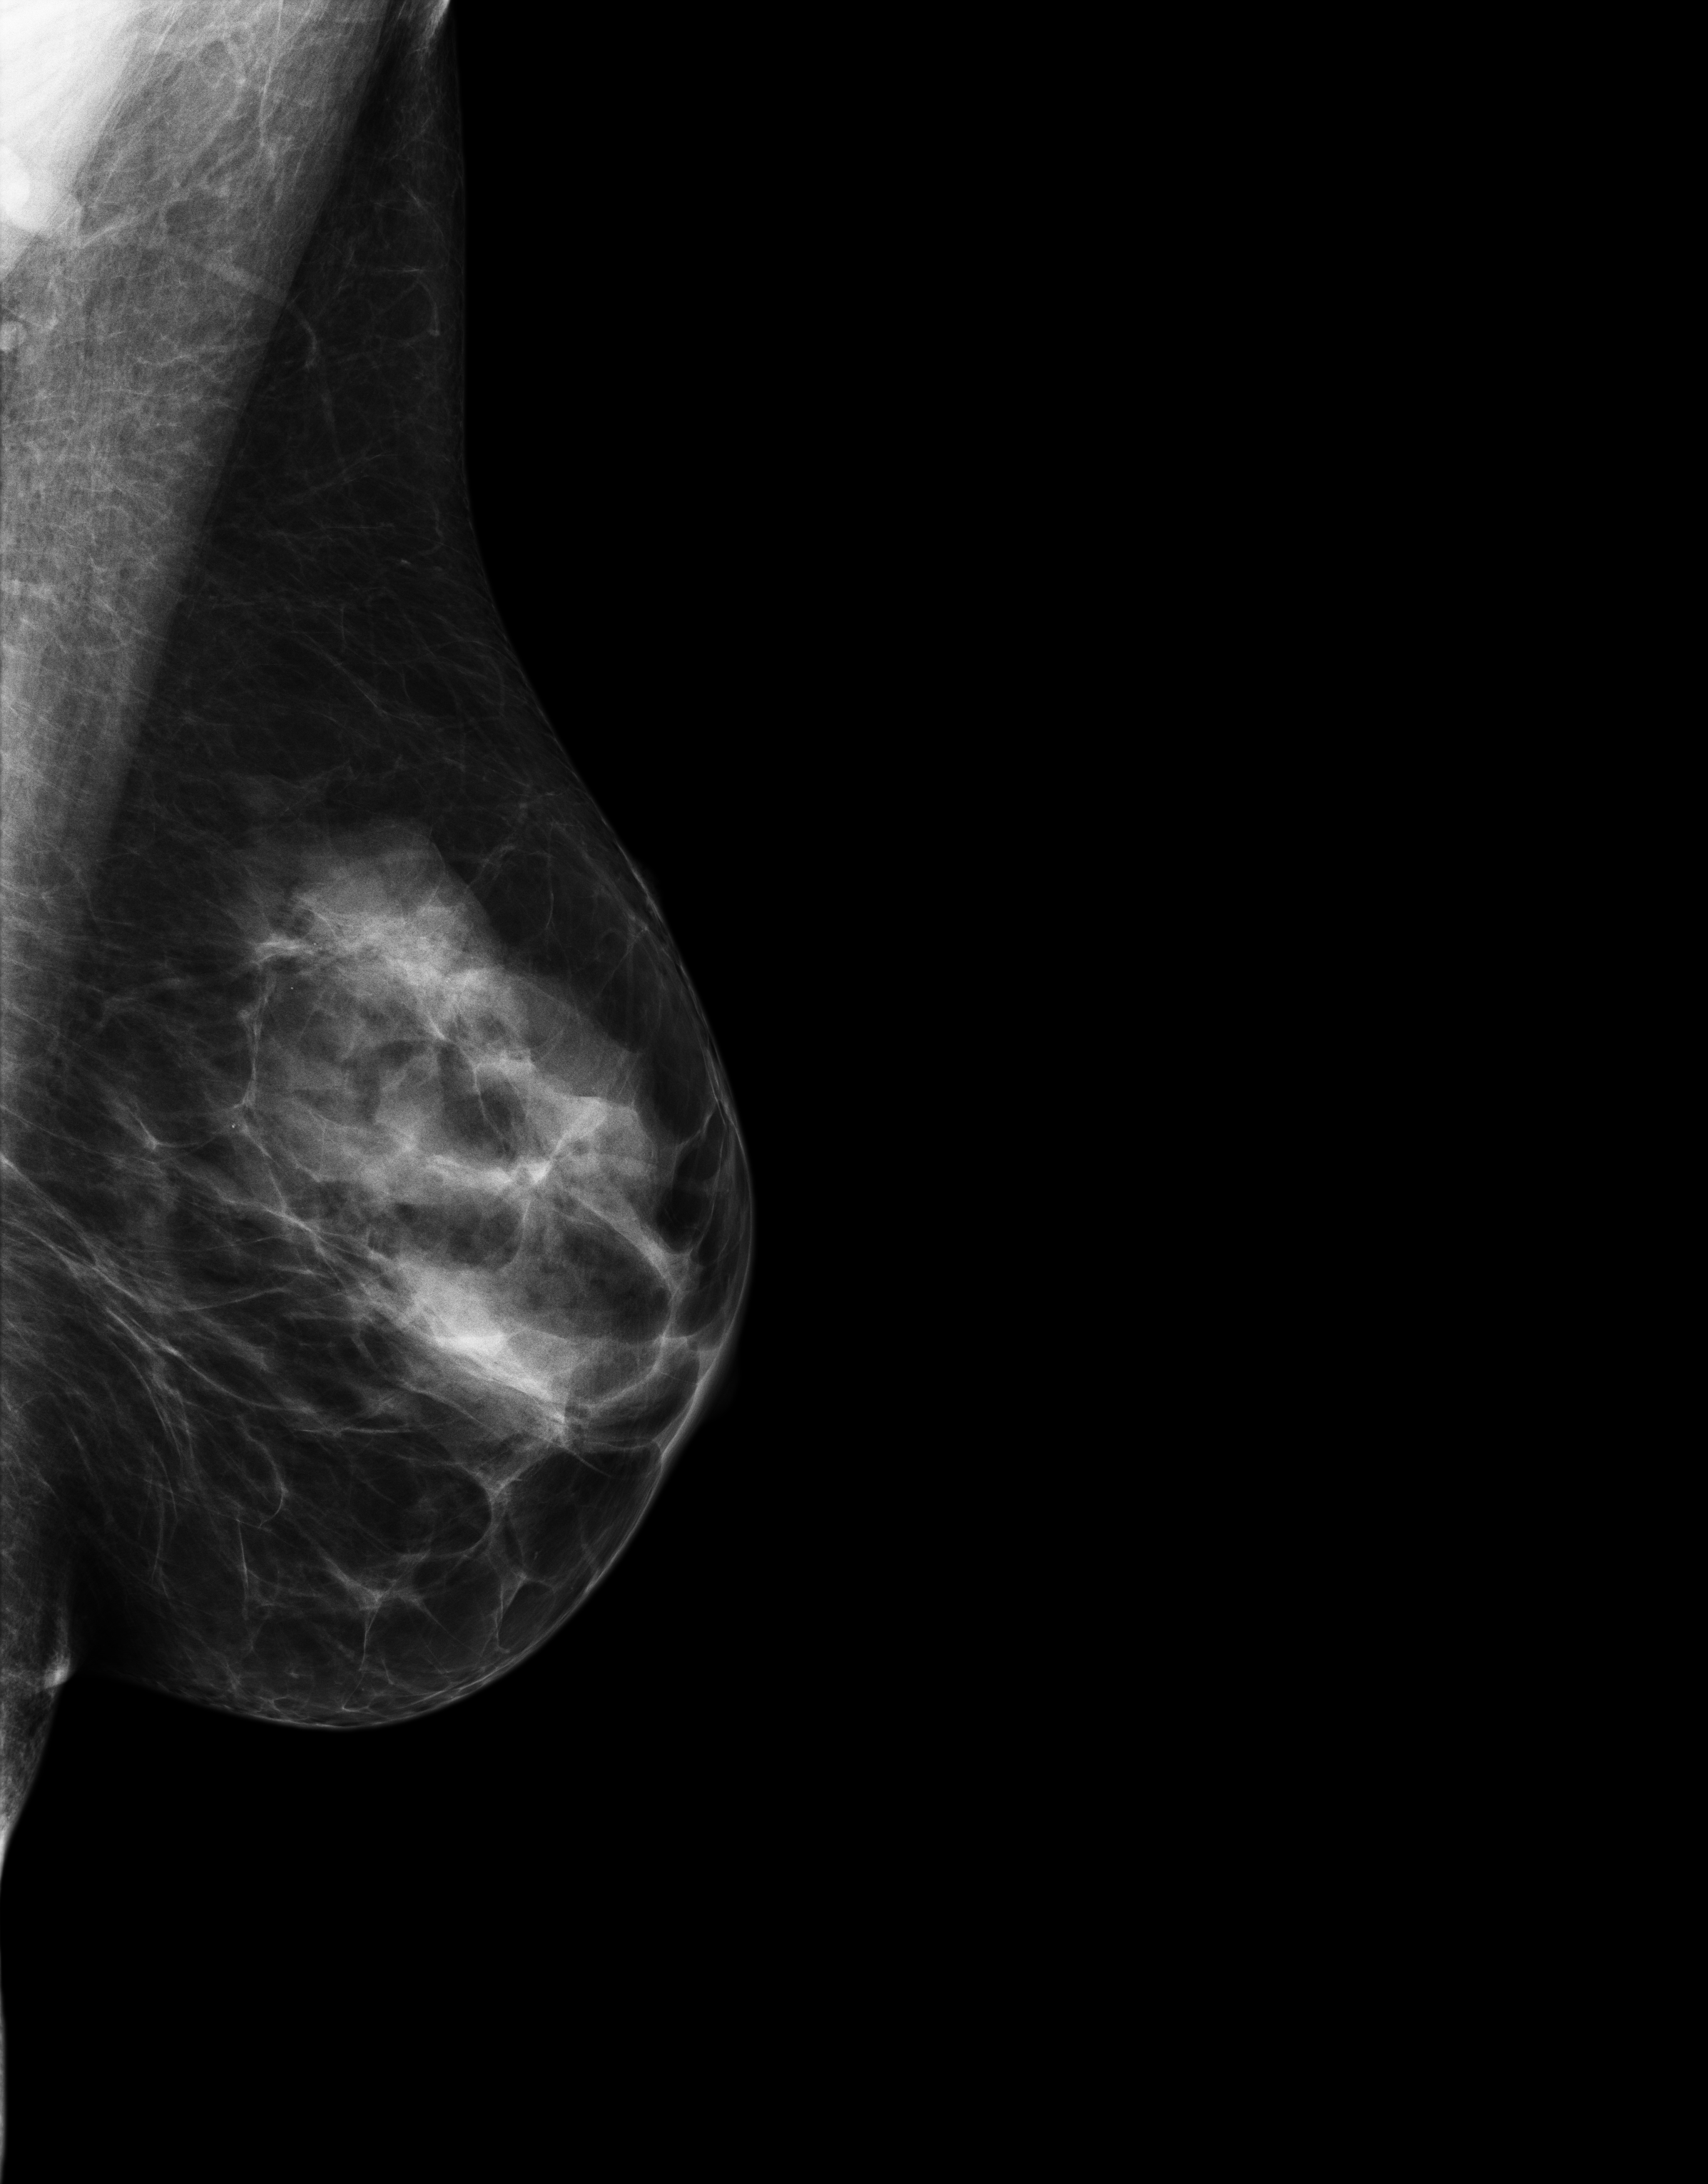
Full-field digital mammogram (FFDM); left breast; mediolateral oblique (MLO) view; annual screening mammography examination. Female patient, age 51 years.
Breast density at the screening exam (both breasts): heterogeneously dense (BI-RADS density category c). Final BI-RADS assessment for this screening round (tomosynthesis exam, both breasts): category 1. Recall: no recall after this screen.